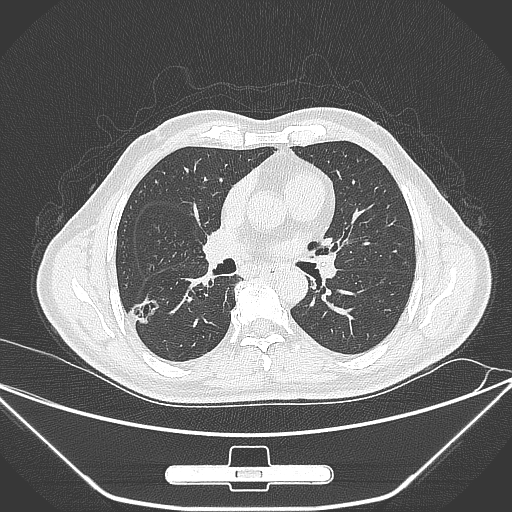
Chest CT, one axial slice; position 153 of 310 along the scan axis; lung window (W 1500 / L -600 HU); 1 mm slice thickness; 512 × 512 image matrix, field of view 398 × 398 mm. Male patient, age 71 years. From the clinical record (not read from this slice): clinical TNM (as recorded): T1c N0 M0.
Structures marked on this image (bounding box drawn by a radiologist):
- lung tumour (recorded histology: adenocarcinoma): bounding box [x1, y1, x2, y2] px = [126, 289, 168, 327]